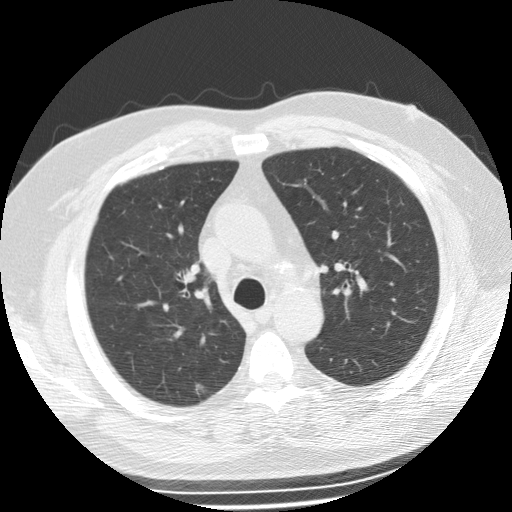
Axial slice from a low-dose chest CT screening exam, second screening round (one year after baseline), lung window (W 1500 / L -600 HU), 2.5 mm slice thickness, standard (soft-tissue) reconstruction kernel (STANDARD), slice 117 of 165 in the series. Male, age 62 years at enrolment.
- Expert reader's lesion annotation, bounding box (x1, y1, x2, y2) in pixels: (180, 379, 221, 403).
- Reader record for this screening exam (exam-level; its link to the box is not recorded): non-calcified nodule or mass ≥4 mm, right upper lobe, 6 × 4 mm, poorly defined margins, ground glass attenuation, pre-existing on the prior screen: yes; interval growth: no.
- Lung cancer was diagnosed 405 days after this screen: bronchiolo-alveolar adenocarcinoma, NOS, right upper lobe, well differentiated (G1), stage IA (AJCC 6th edition), 12 mm at pathology.